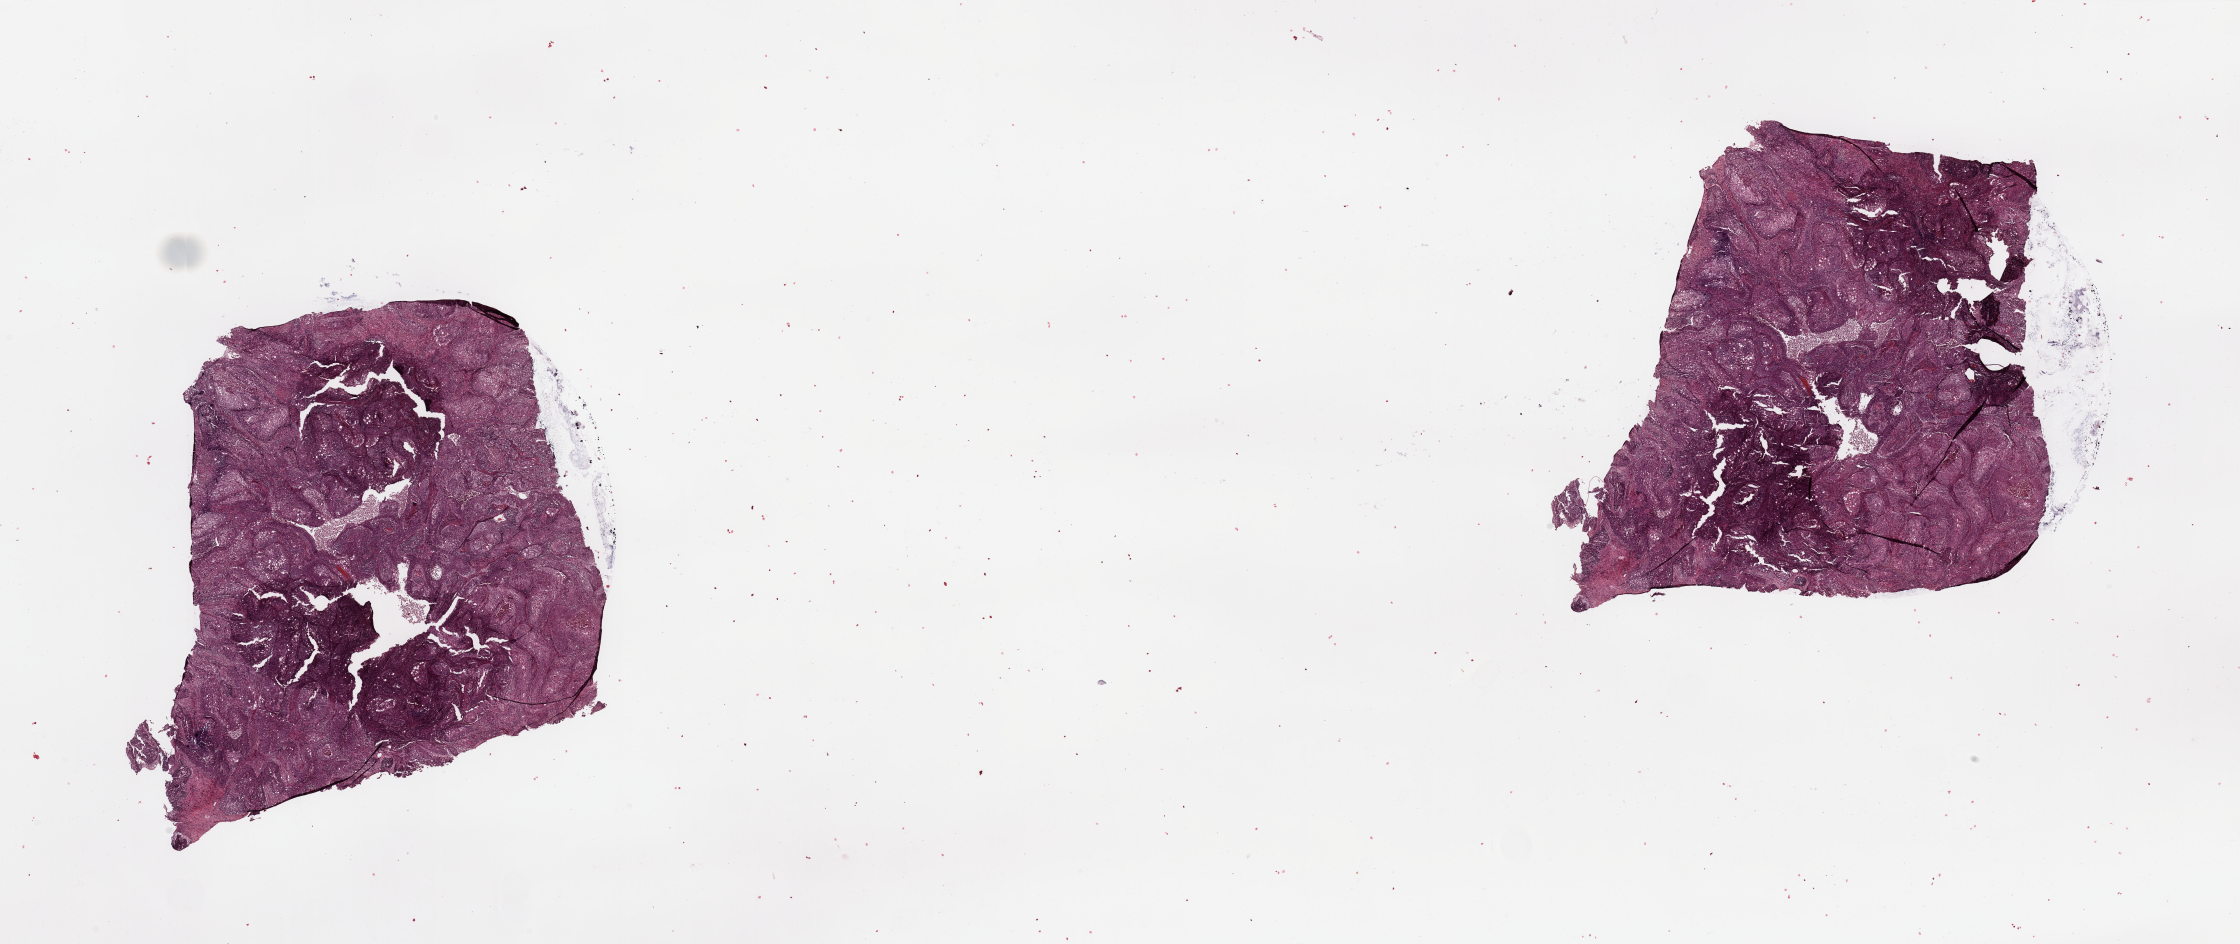
Hematoxylin and eosin (H&E) stained whole-slide image, shown as a low-resolution overview of the whole scanned area (about 35.4 x 14.9 mm), lung, tumour tissue. 68-year-old male patient.
Patient diagnosis (cohort enrolment): squamous cell carcinoma (lung).